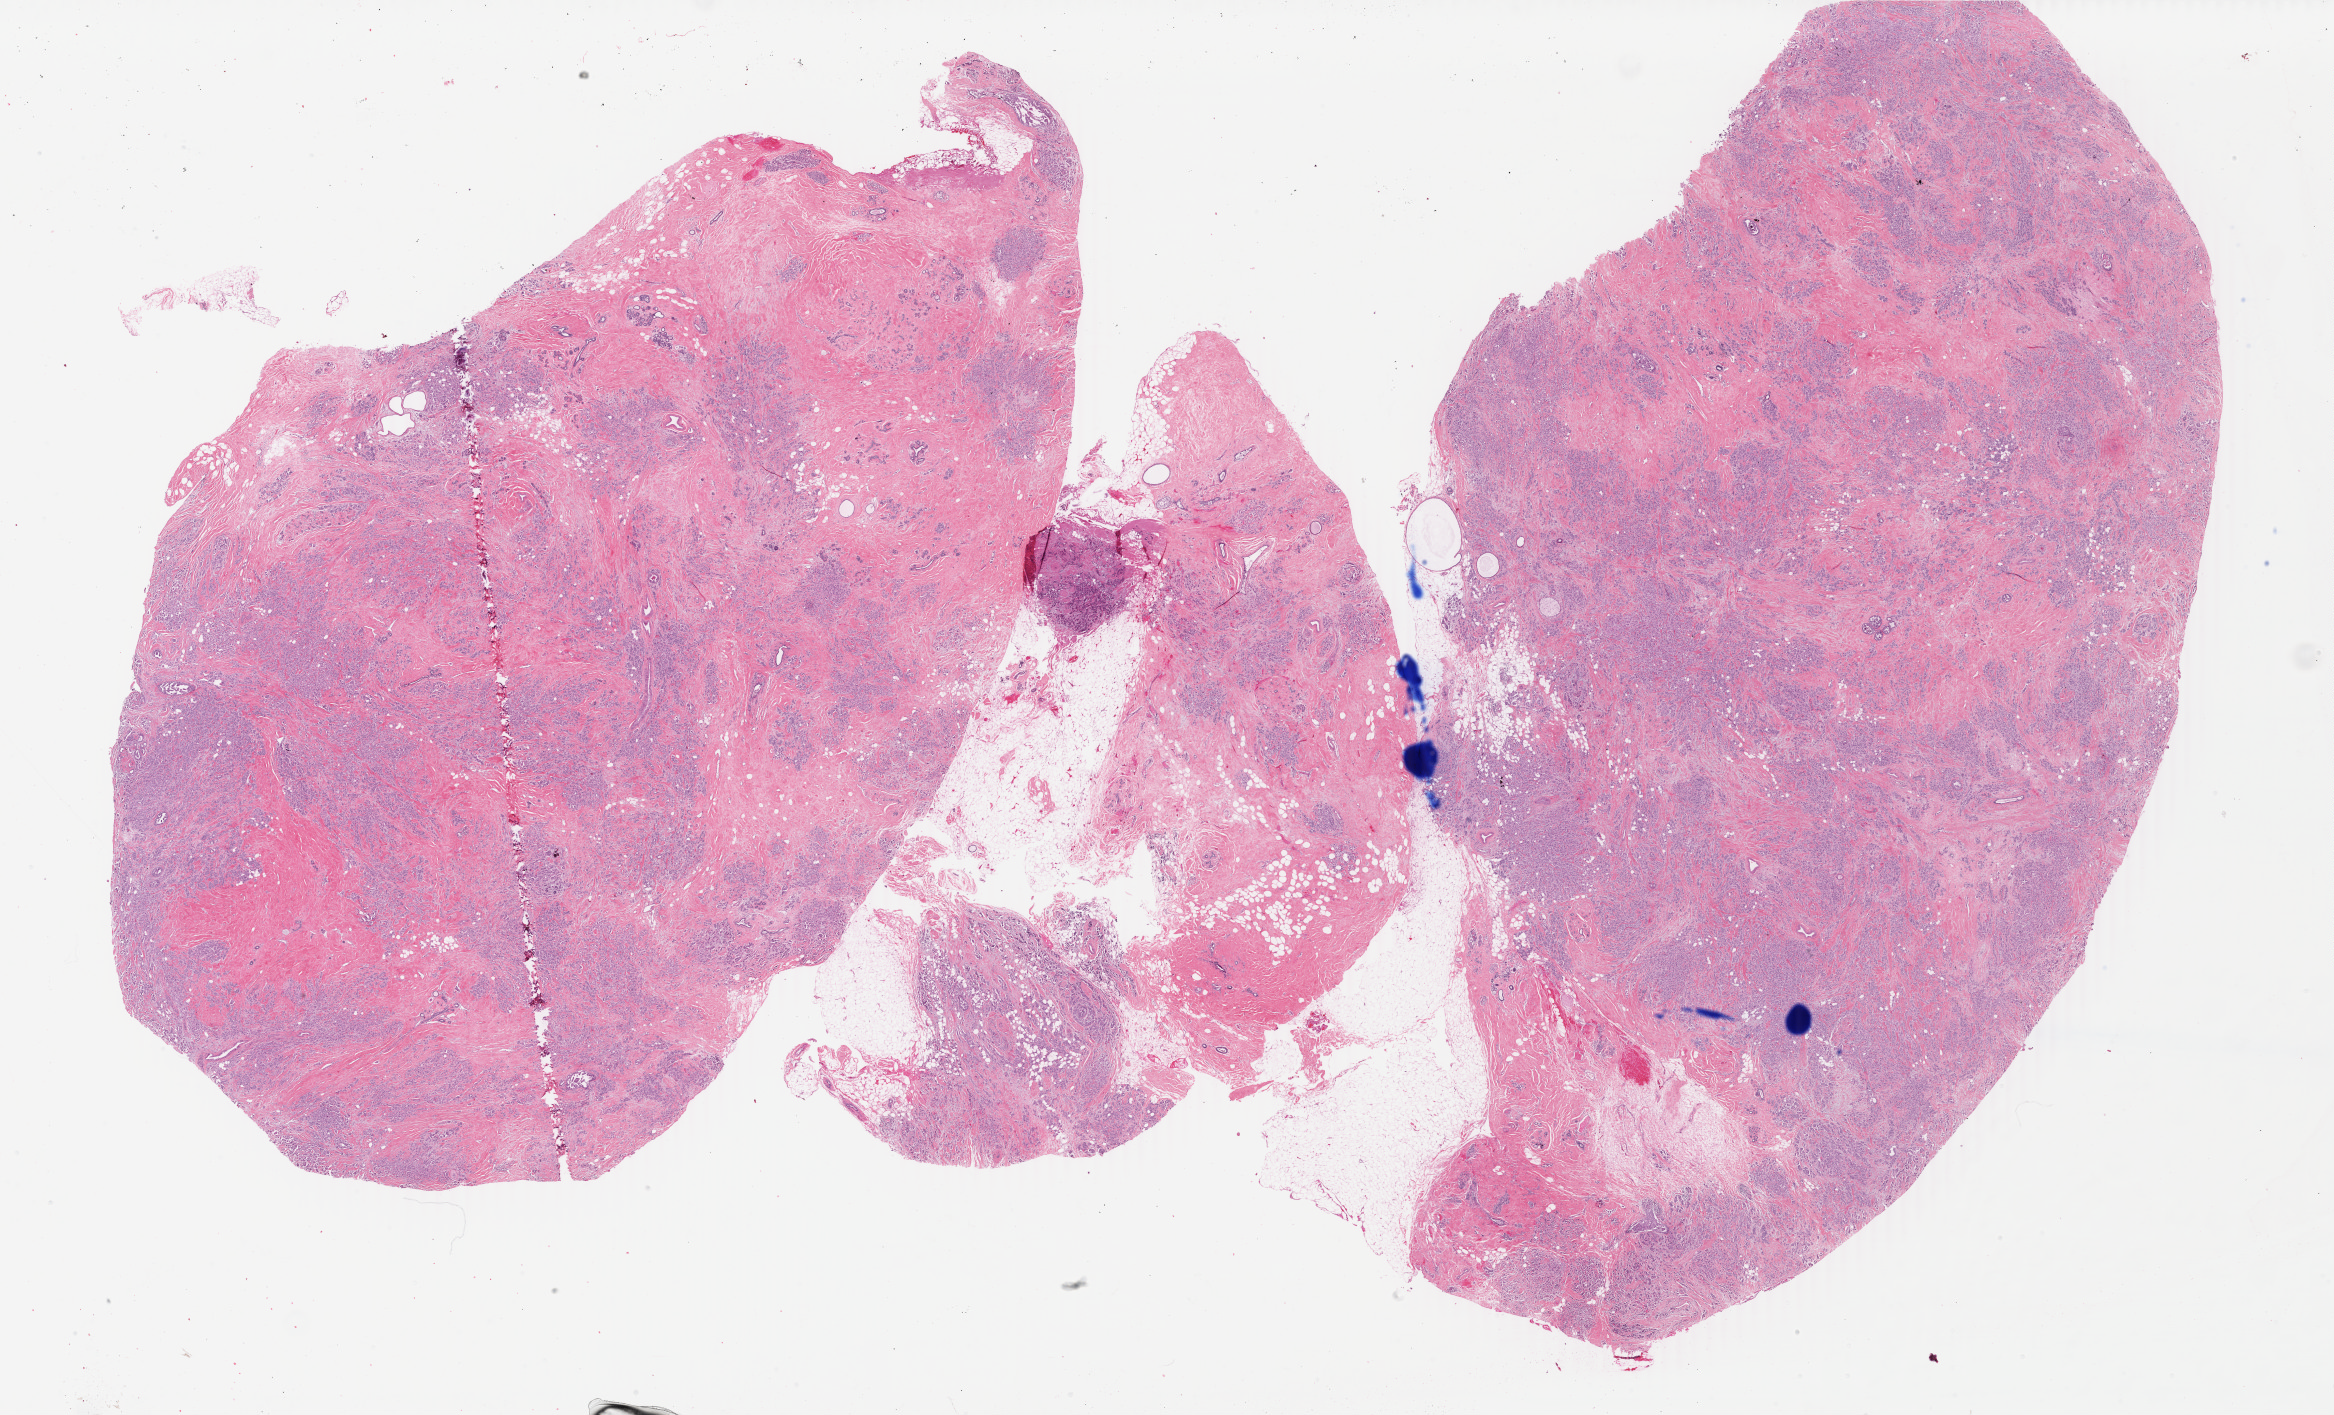
H&E whole-slide image — shown as a low-resolution overview of the whole scanned area (about 37.1 x 22.5 mm). FFPE section. Primary tumour sample from the breast. Female patient; age at initial diagnosis 46 years.
• laterality: right
• pathologic diagnosis: Infiltrating duct carcinoma, NOS